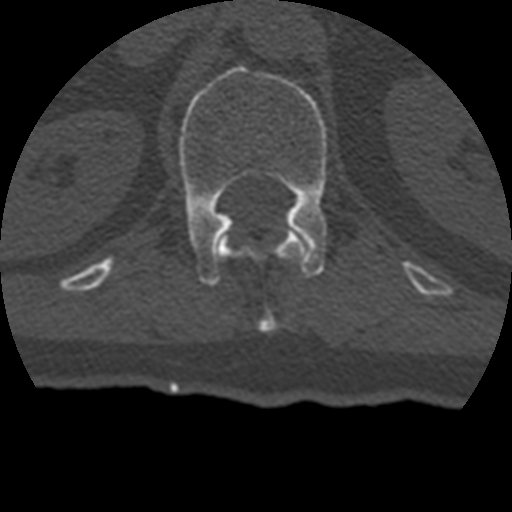
CT including the spine, one axial slice; slice 156 of 399 in the series (ordered by position); reconstruction kernel STANDARD; bone window (W 1800 / L 400 HU); 512 × 512 image matrix. Patient age 69 years. From the clinical record (not read from this slice): primary cancer: prostate.
Annotated regions visible in this slice (semi-automatically segmented with operator editing):
- L1 vertebra: box from (x=179, y=65) to (x=329, y=286) px
- T12 vertebra: (x=219, y=230)–(x=309, y=333)